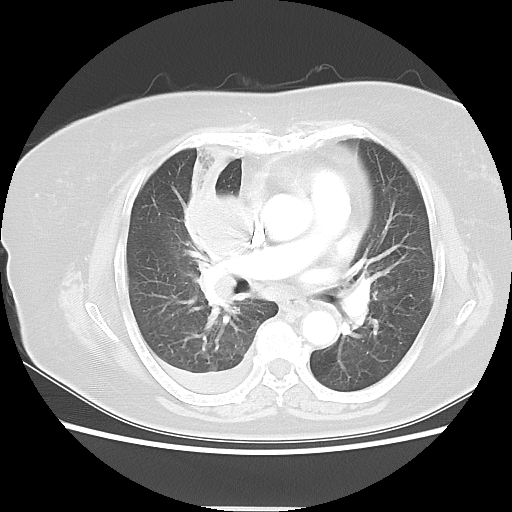
Chest CT, one axial slice. Slice 26 of 48 in the series (ordered by position). Reconstruction kernel LUNG. 120 kVp. Lung window (W 1500 / L -600 HU). 5 mm slice thickness. 512 × 512 image matrix, field of view 360 × 360 mm. Female patient, age 73 years. From the clinical record (not read from this slice): clinical TNM (as recorded): T3 N3 M1b.
Annotated regions visible in this slice (rectangle marked by the reading radiologist):
- lung tumour (recorded histology: small cell carcinoma): bounding box (x1, y1, x2, y2) in pixels: (187, 139, 261, 313)